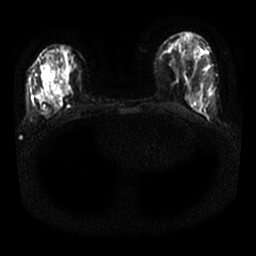
Breast MRI, one axial slice. Position 7 of 25 along the scan axis. Diffusion-weighted series; image 2 of 4 stored at this slice position (different b-values; order by instance number). 1.5 T. 4 mm slice thickness. 256 × 256 image matrix, field of view 330 × 330 mm. Female patient.
Outlined on this slice (outlined manually by an expert reader):
- tumour on diffusion-weighted imaging: bounding box [x1, y1, x2, y2] px = [57, 83, 70, 95]